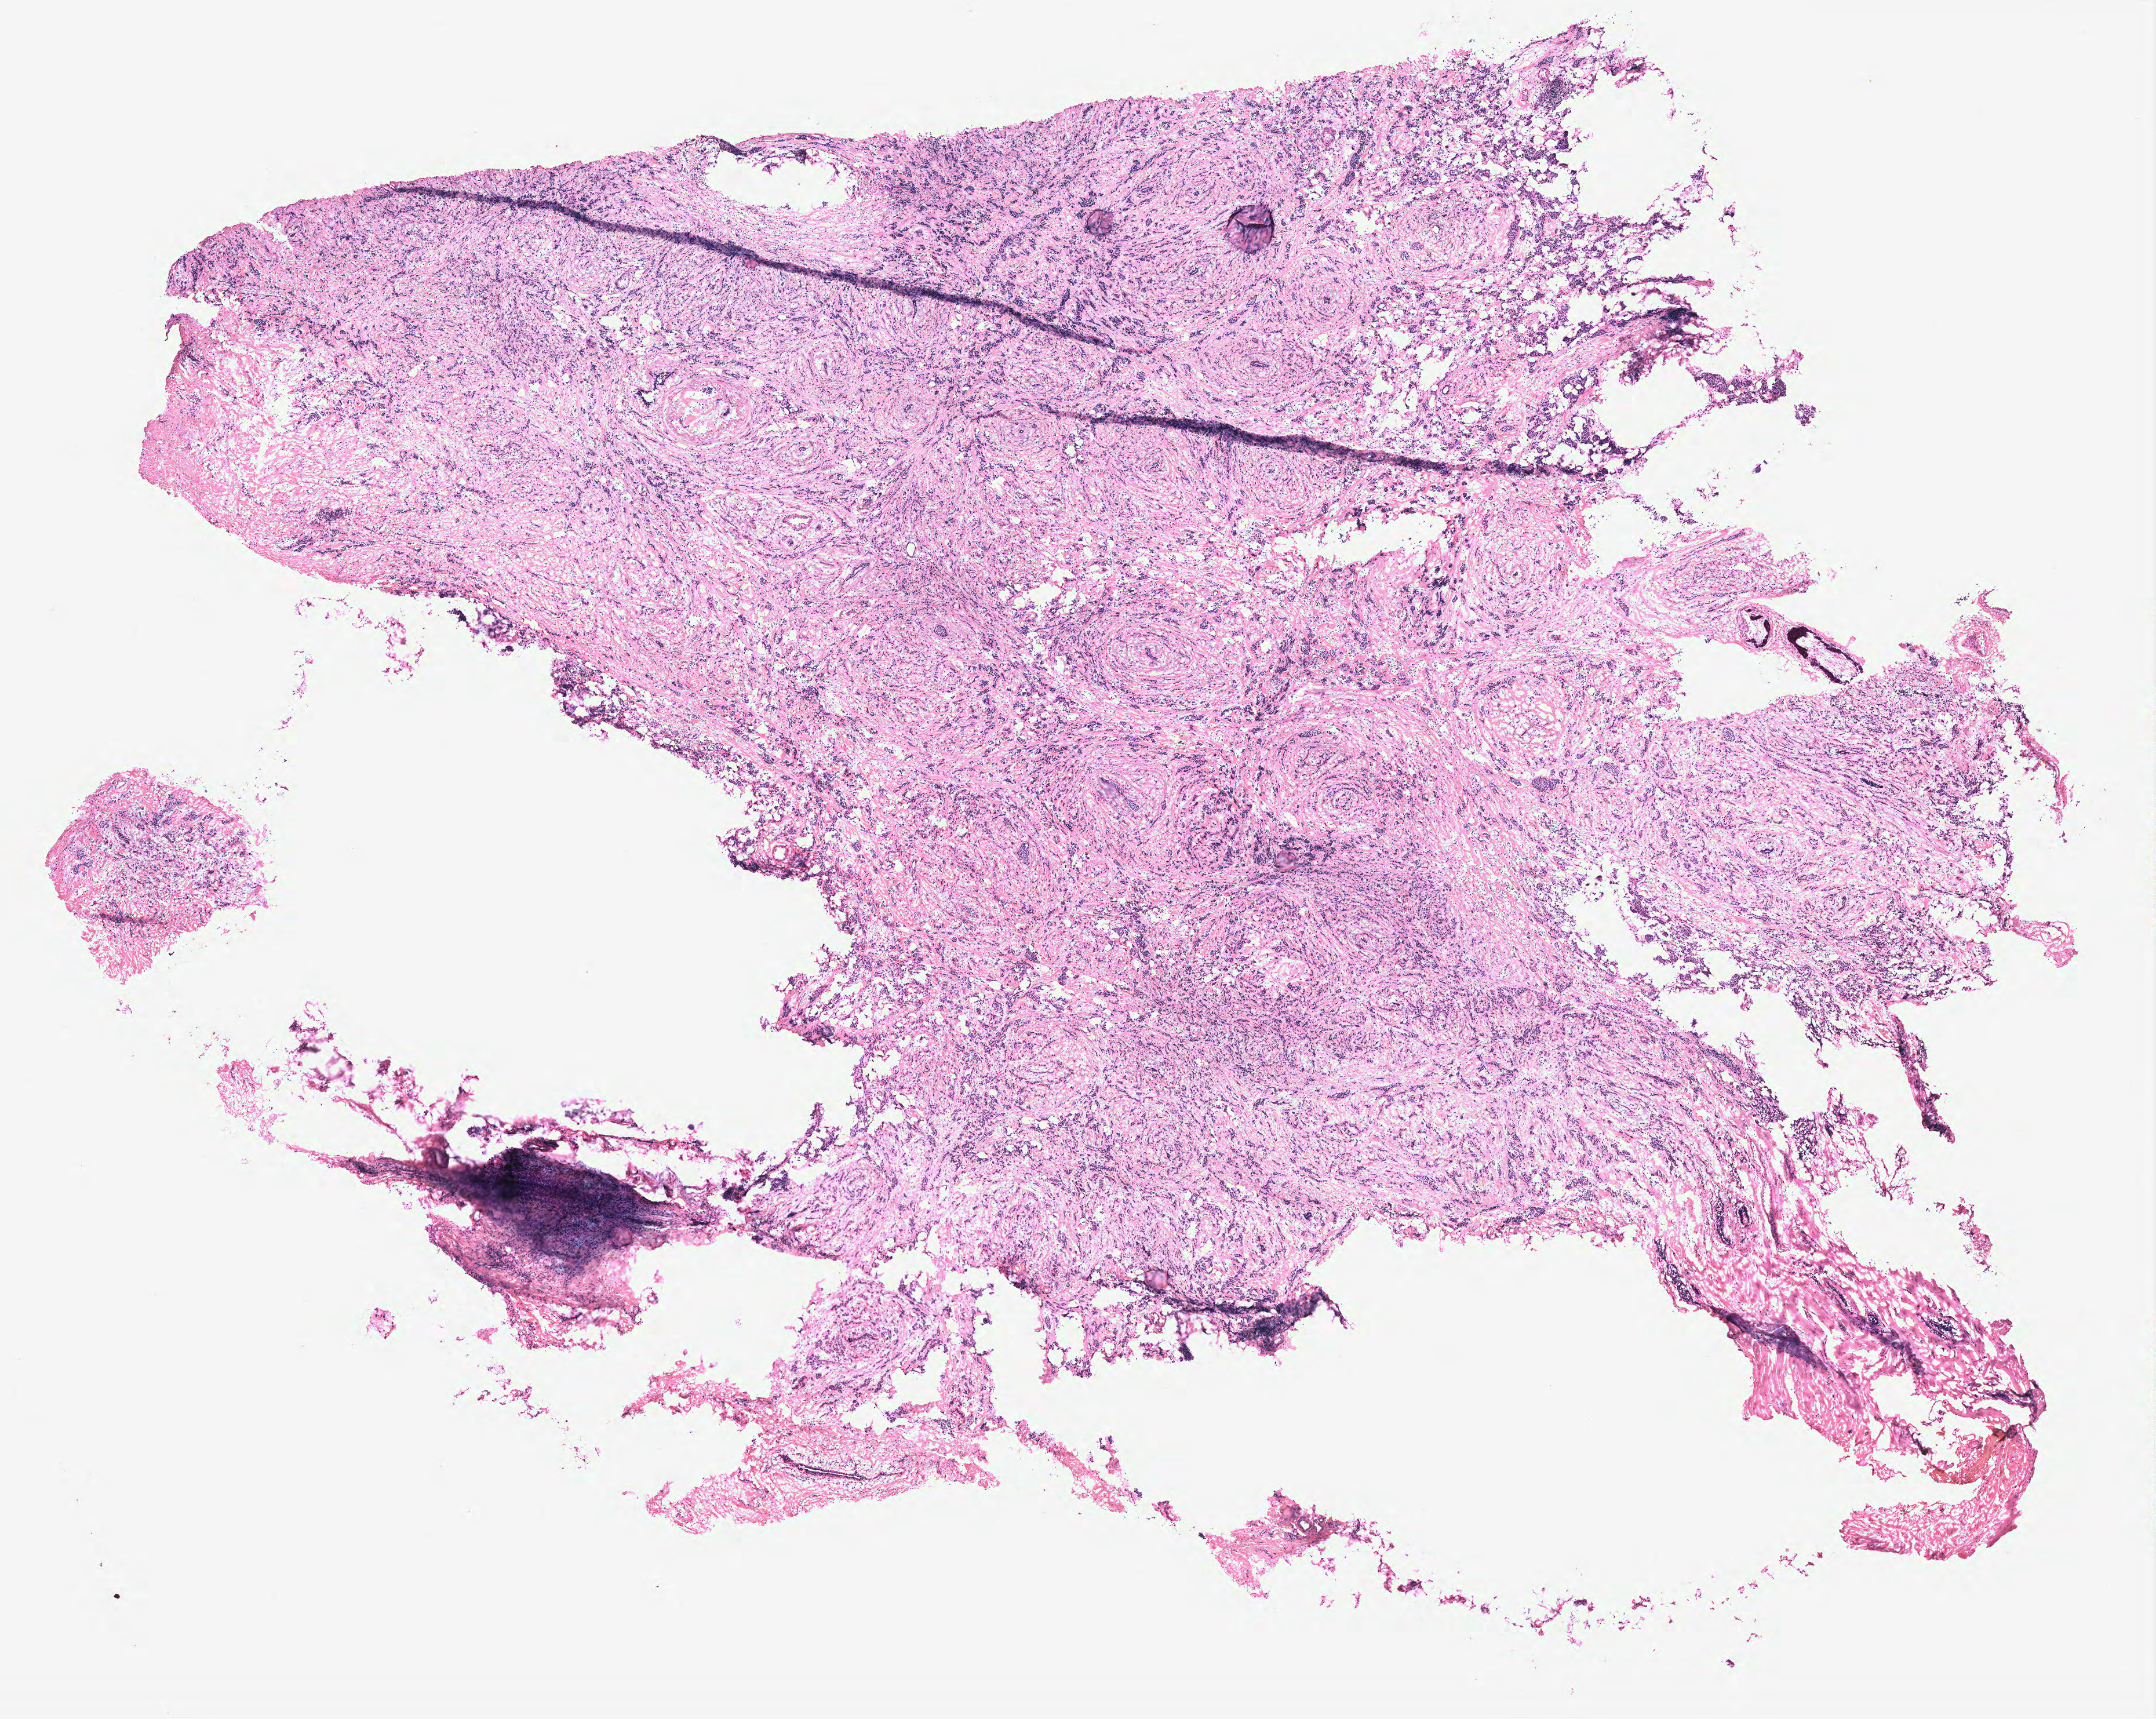
Whole-slide histology image, Hematoxylin and eosin (H&E) stained, shown as a low-resolution overview of the whole scanned area (about 14.9 x 11.9 mm). Breast, tissue type not recorded. Female, 70 y/o.
Patient diagnosis: Infiltrating duct carcinoma, NOS.